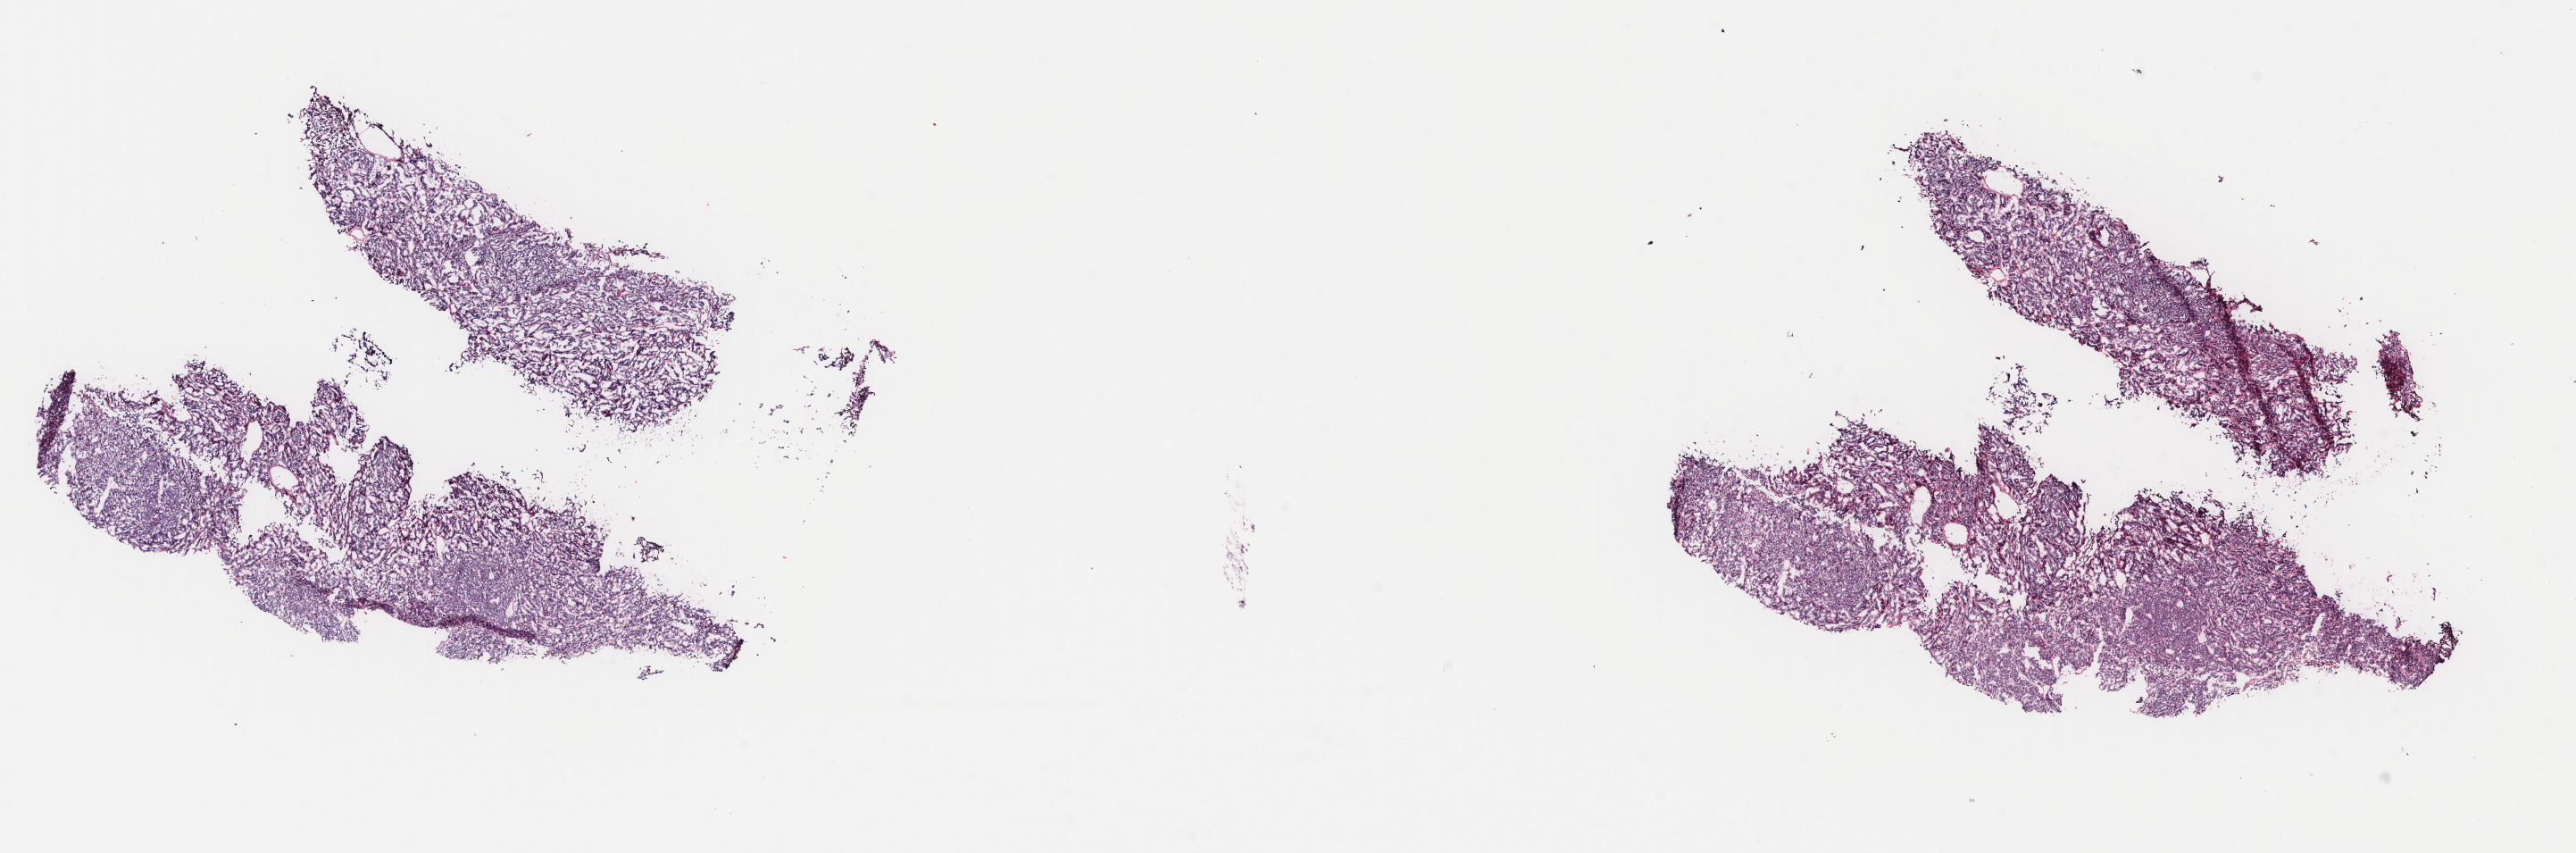
Whole-slide histology image, Hematoxylin and eosin (H&E) stained, whole scanned area (about 22.9 x 7.6 mm) shown as a low-resolution overview; frozen section from the top of the tissue portion; sample: primary tumour, thyroid. Patient: male, age at initial diagnosis 25 years. Slide review estimates, as recorded: tumour cells 100%, tumour nuclei 95%, normal cells 0%, stromal cells 0%, necrosis 0%. Inflammatory infiltration, as recorded: lymphocyte infiltration 0%, monocyte infiltration 0%, neutrophil infiltration 0%.
Diagnosis: Papillary adenocarcinoma, NOS (thyroid gland). AJCC pathologic stage: I.